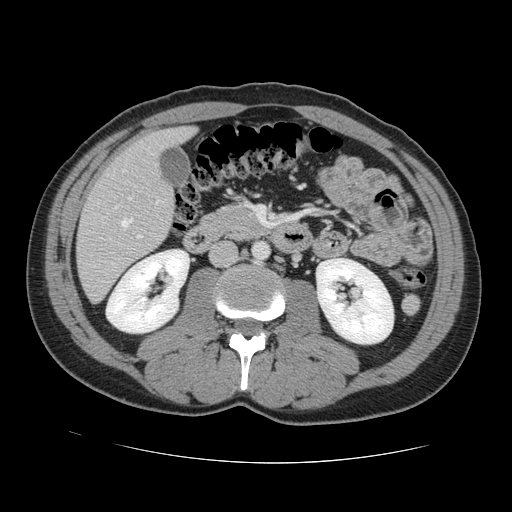
Contrast-enhanced abdominal CT, one axial slice. Slice 47 of 131 in the series (ordered by position). Intravenous contrast given. Soft-tissue window (W 400 / L 40 HU). 2.5 mm slice thickness. 512 × 512 image matrix, field of view 380 × 380 mm. Male patient, age 40 years. Case-level facts recorded for this patient, not image findings: diagnosis: colorectal cancer liver metastases, imaged before liver resection; multiple liver metastases: yes; largest metastasis: 2.9 cm; chemotherapy before resection: yes.
Structures marked on this image (expert manual segmentation):
- hepatic veins: bounding box [x1, y1, x2, y2] px = [121, 219, 132, 227]
- liver: [78, 128, 192, 302]
- planned liver remnant (the part of the liver to remain after resection): [124, 128, 193, 167]
- portal vein (with intrahepatic branches): [129, 197, 142, 238]